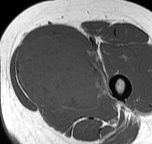
MRI of an extremity soft-tissue mass, one axial slice. Slice 27 of 57 in the series (ordered by position). MR volume resampled by the dataset authors to the PET/CT grid (not the native acquisition matrix). 3.27 mm slice thickness. 152 × 144 image matrix, field of view 148 × 141 mm. Female patient. From the clinical record (not read from this slice): histological type: pleiomorphic leiomyosarcoma; grade: intermediate; site of the primary tumour: left thigh.
Outlined on this slice (expert contour drawn on MRI and transferred to this co-registered scan by the dataset authors):
- gross tumour volume including surrounding oedema: bounding box <15,35,108,109> (left, top, right, bottom; pixels)
- gross tumour volume (mass): <15,37,105,107>